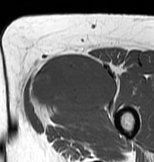
MRI of an extremity soft-tissue mass, one axial slice. Position 33 of 83 along the scan axis. MR volume resampled by the dataset authors to the PET/CT grid (not the native acquisition matrix). 3.27 mm slice thickness. 154 × 162 image matrix, field of view 150 × 158 mm. Female patient. From the clinical record (not read from this slice): histological type: myxofibrosarcoma; grade: intermediate; site of the primary tumour: left thigh.
Outlined on this slice (expert contour drawn on MRI and transferred to this co-registered scan by the dataset authors):
- gross tumour volume including surrounding oedema: bounding box <28,50,120,128> (left, top, right, bottom; pixels)
- gross tumour volume (mass): <30,50,116,110>